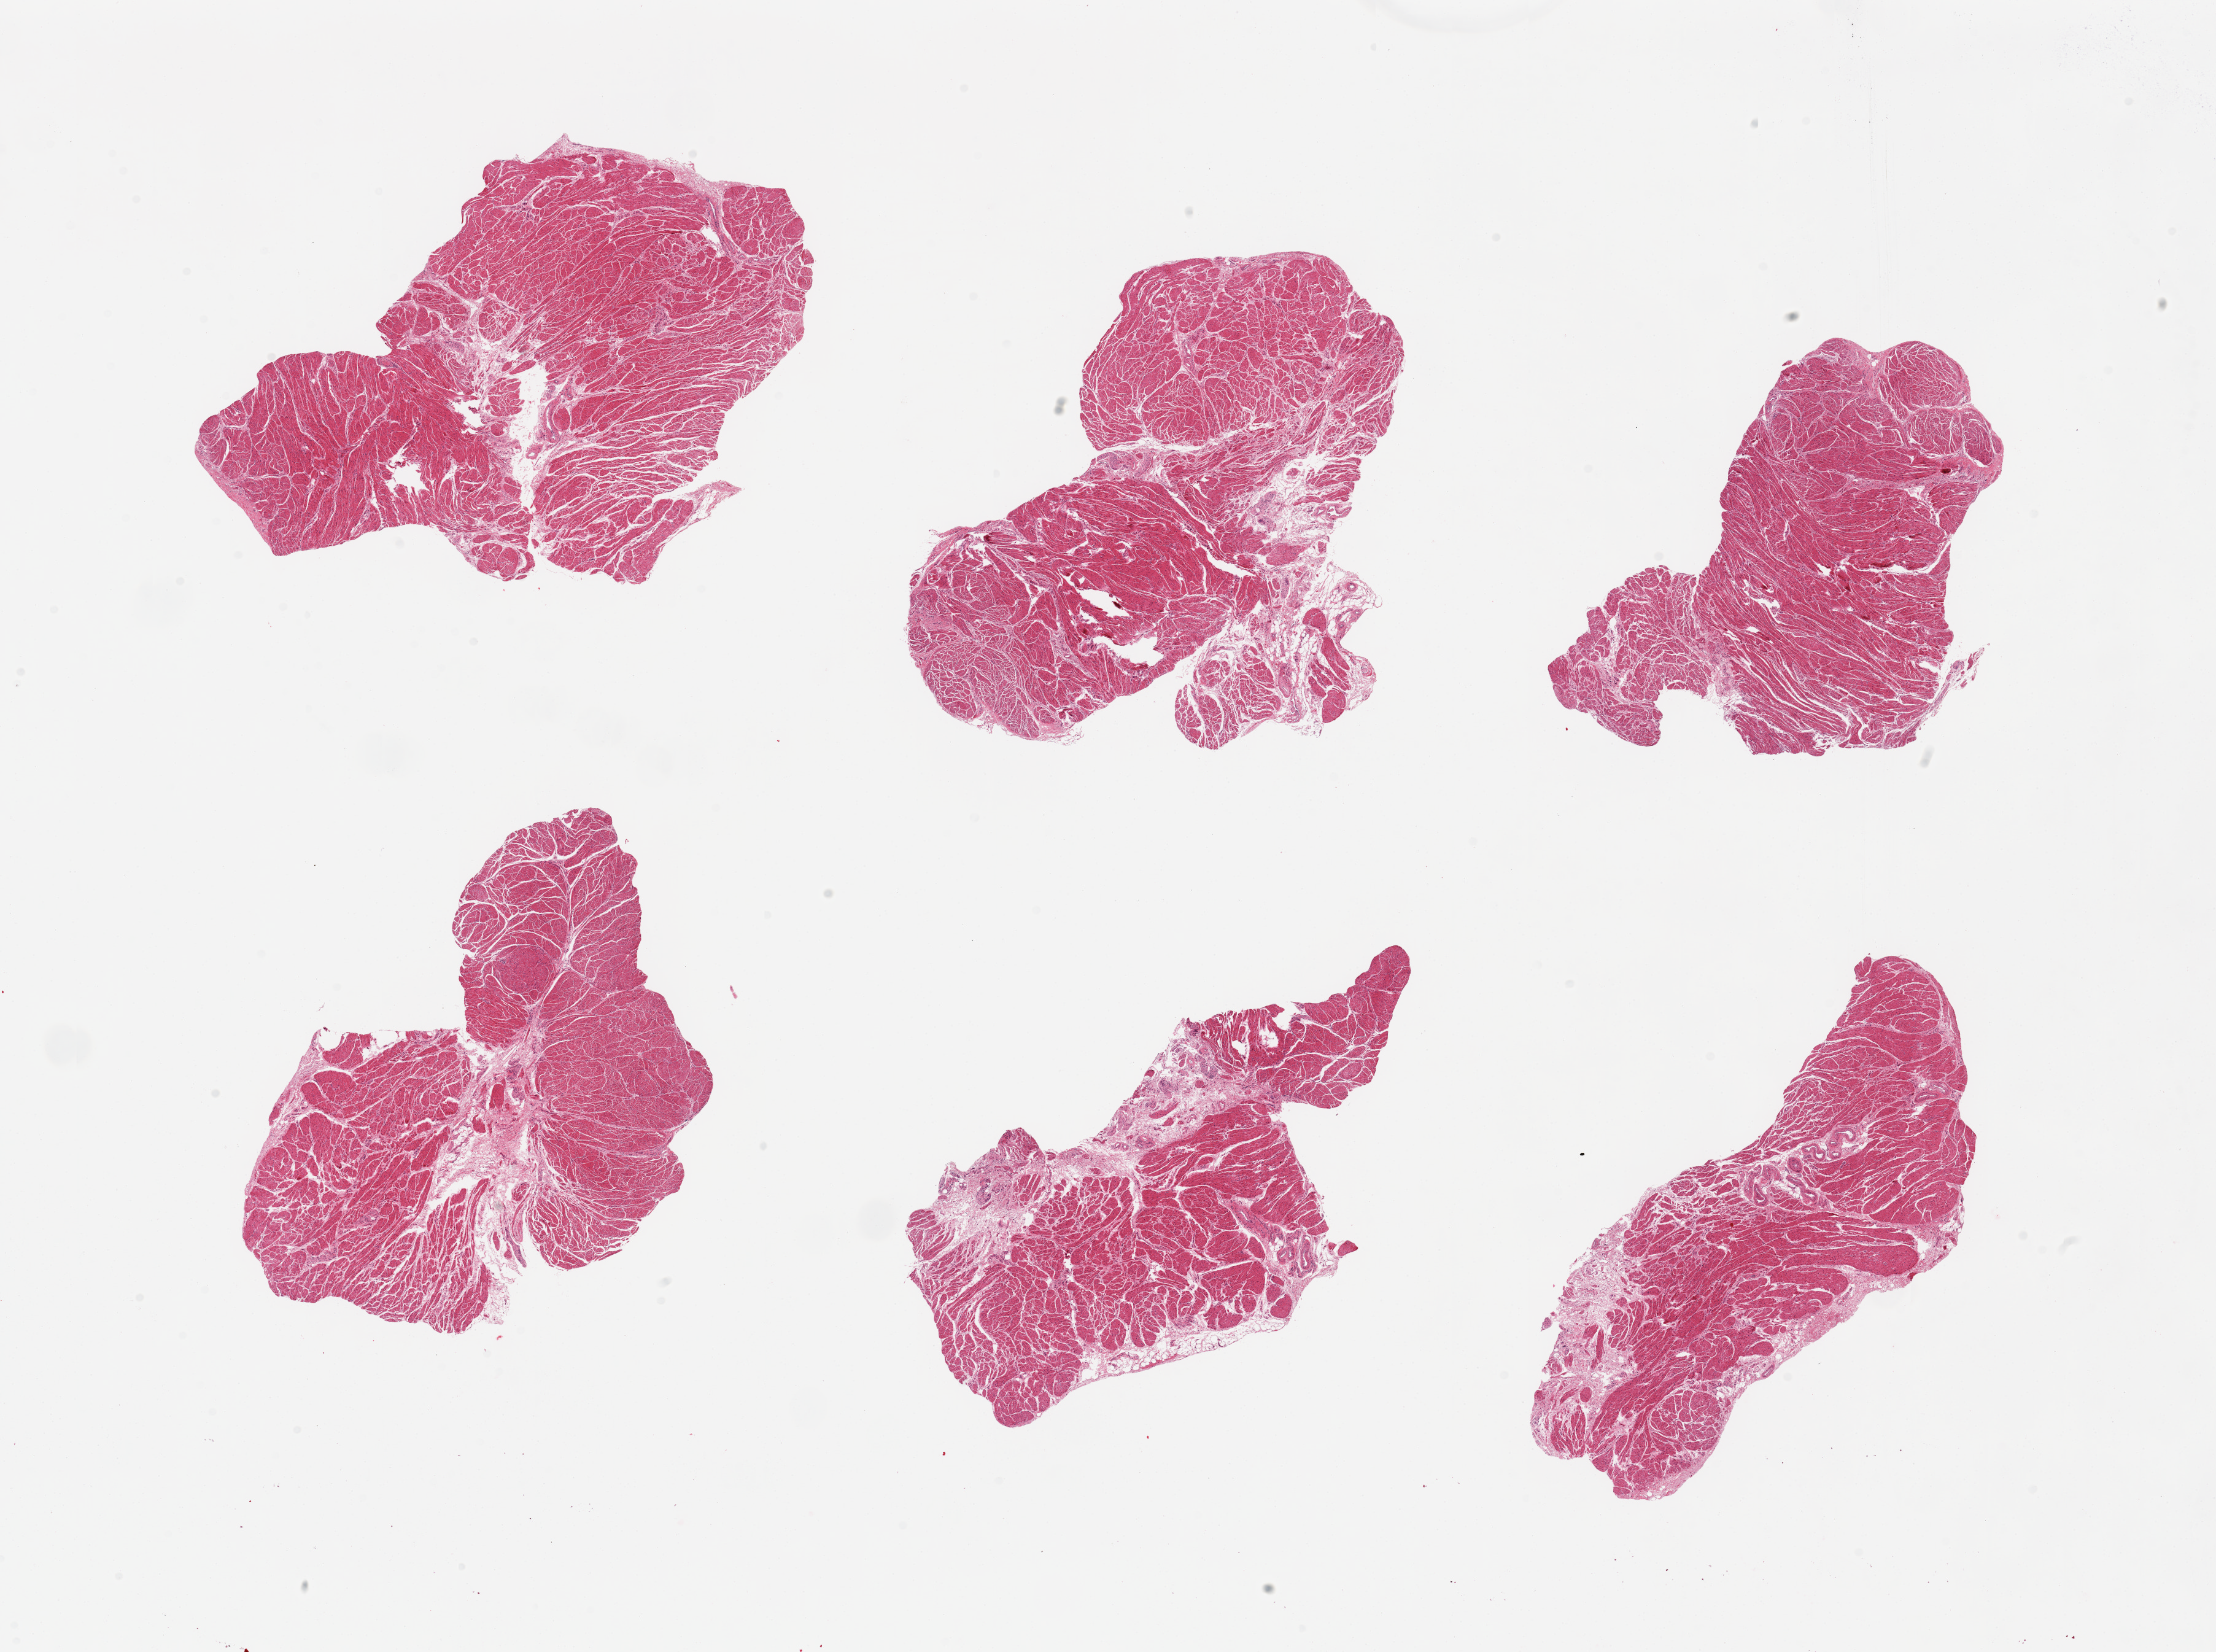
Digitized haematoxylin and eosin-stained section — a low-resolution overview of the entire scanned area, about 28.5 x 21.3 mm, PAXgene-fixed, paraffin-embedded tissue, target tissue: gastroesophageal junction, tissue donor sample. Donor: male.
Review note (as recorded): 6 pieces, all muscularis.